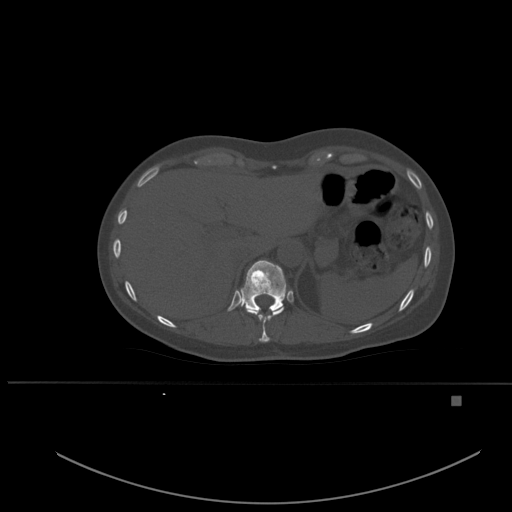
CT including the spine, one axial slice. Slice 279 of 651 in the series (ordered by position). Bone window (W 1800 / L 400 HU). 1.5 mm slice thickness. 512 × 512 image matrix, field of view 443 × 443 mm. Female patient, age 49 years. Case-level facts recorded for this patient, not image findings: primary cancer: breast.
Structures marked on this image (semi-automatic segmentation, software-assisted and operator-edited):
- T10 vertebra: bounding box (x1, y1, x2, y2) in pixels: (246, 306, 285, 342)
- T11 vertebra: (240, 260, 286, 313)